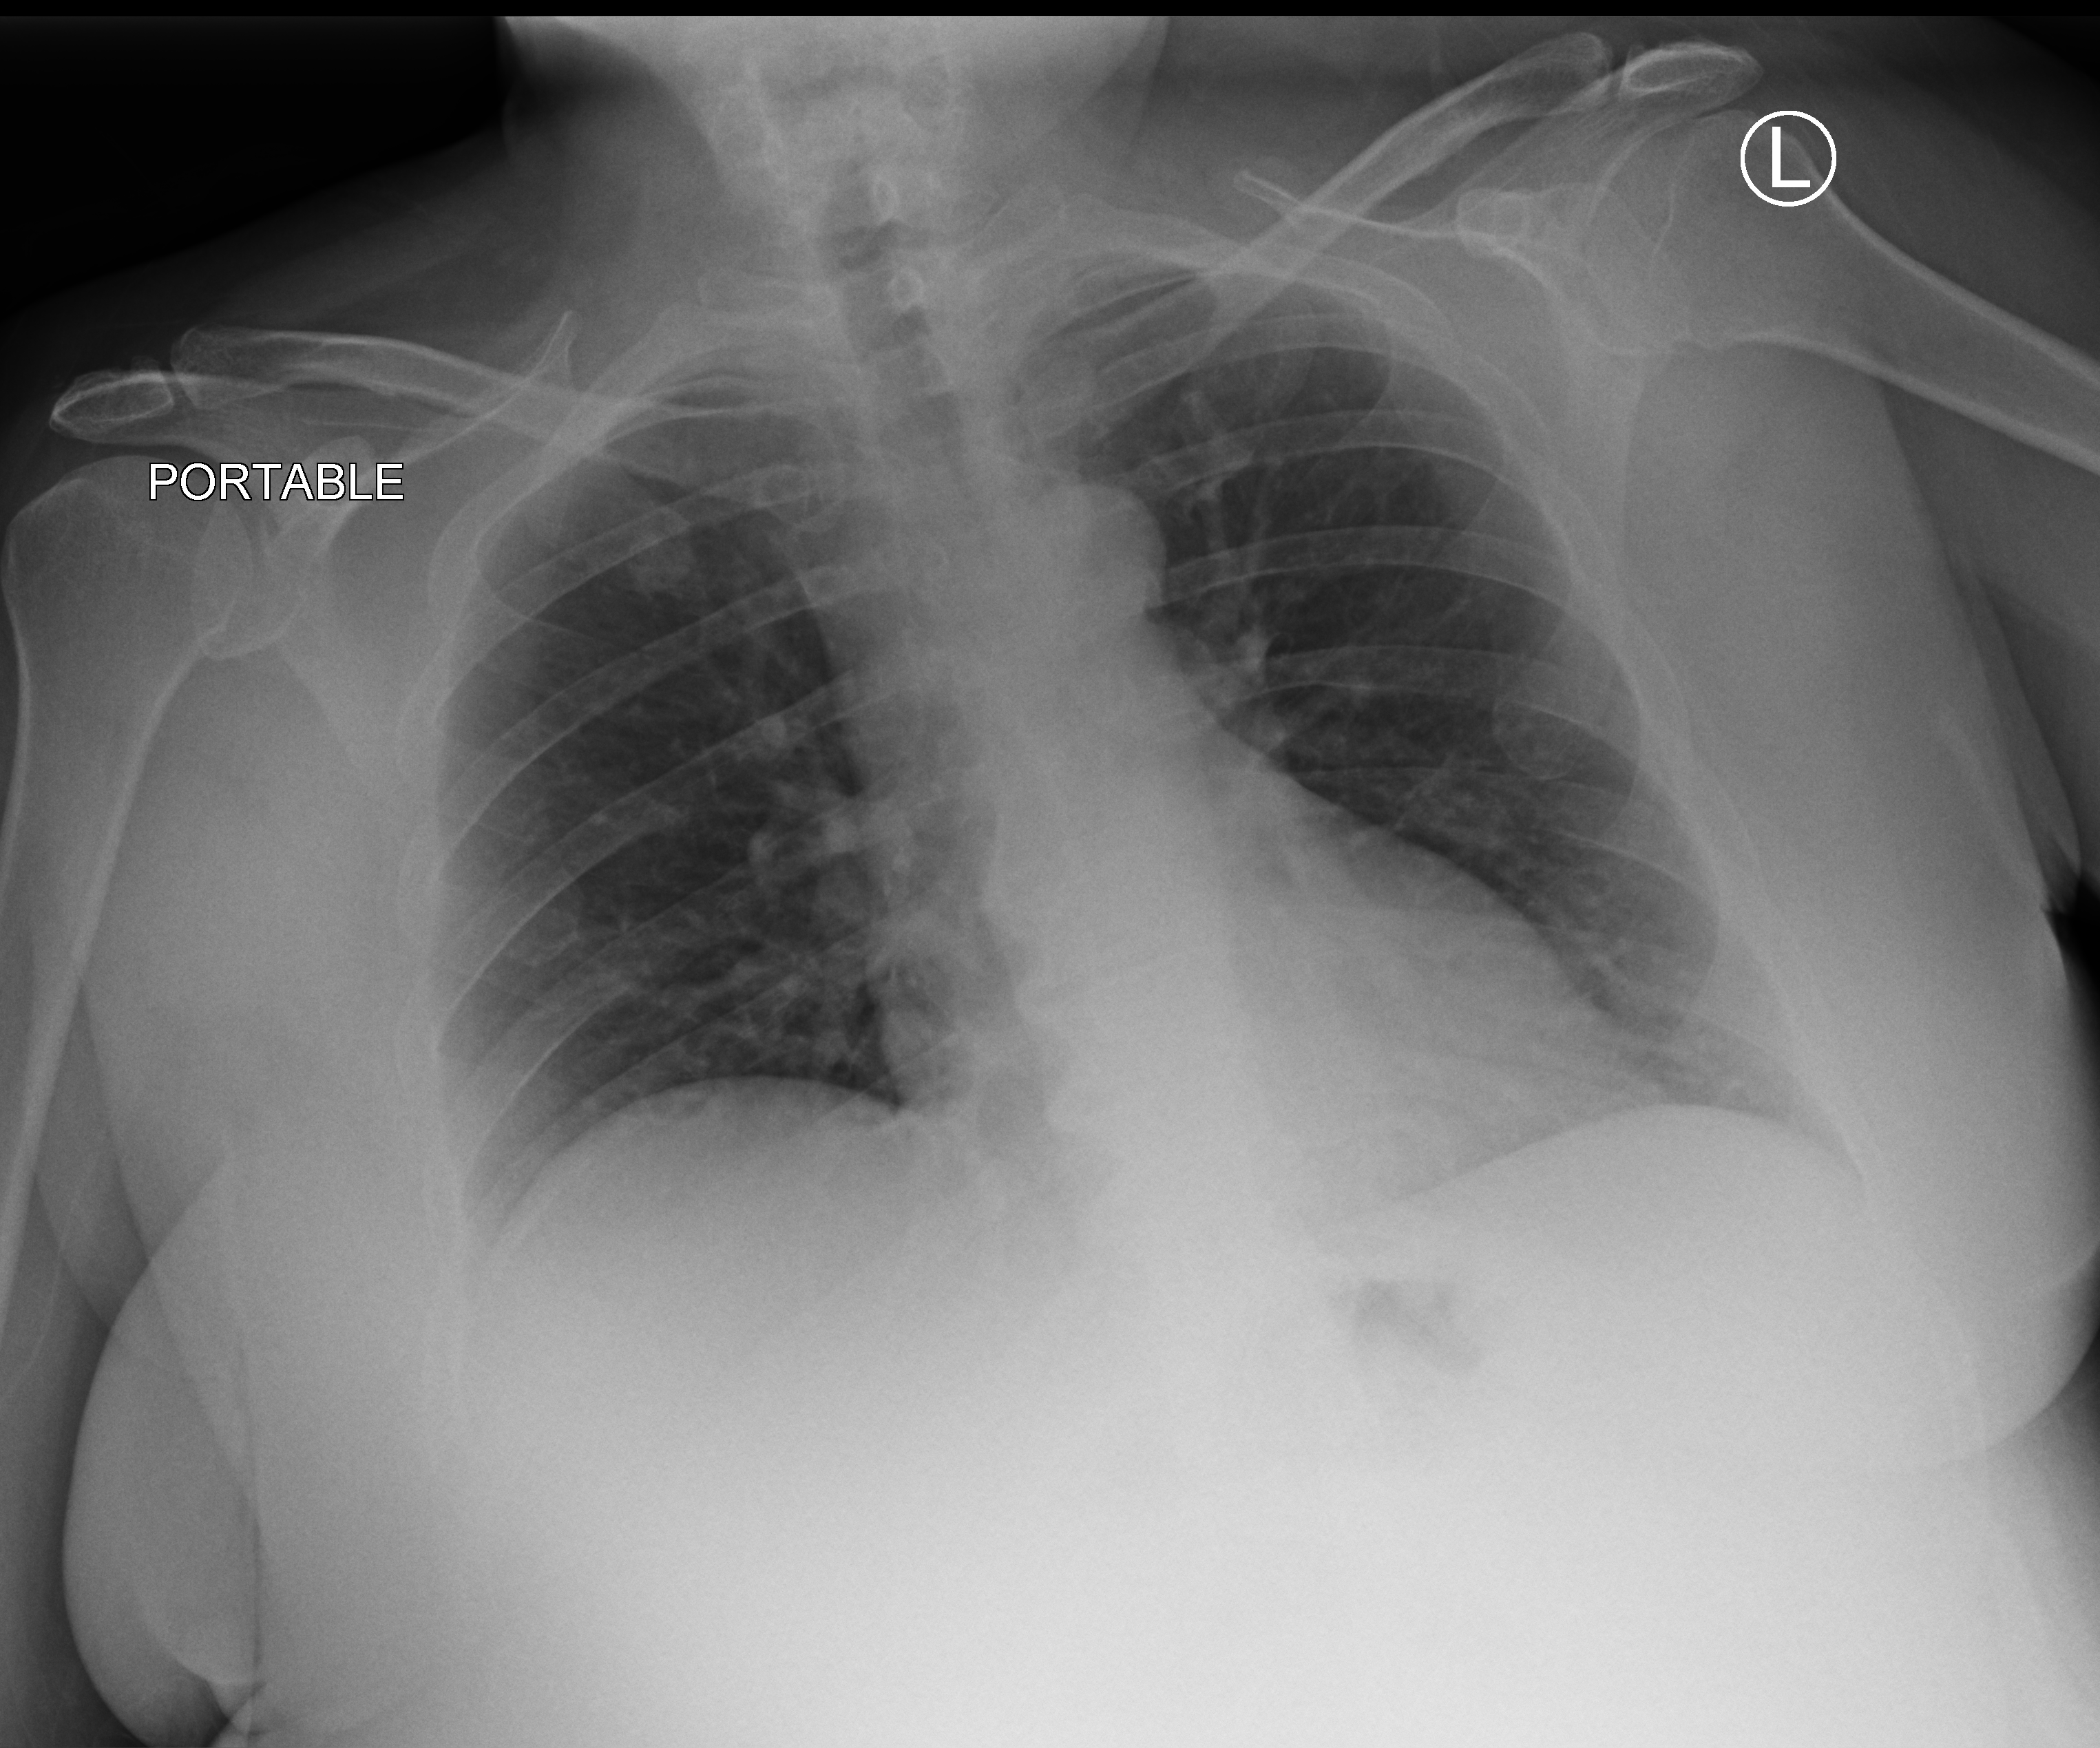
Portable chest radiograph, anteroposterior (AP) projection. Patient hospitalised with COVID-19; female, aged 18–59 years.
Hospital-stay facts (about this admission, not read from this image; timing relative to this image not recorded):
- mechanically ventilated during this hospital stay: no
- length of hospital stay: 2 days